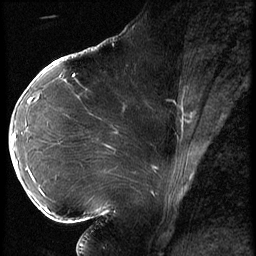
Breast MRI (dynamic contrast-enhanced), one sagittal slice. Slice 32 of 62 in the series (ordered by position). 3 images stored at this slice position (order not interpretable as contrast timing). 1.5 T. TE 4.2 ms, TR 9 ms. 256 × 256 image matrix, field of view 180 × 180 mm. Patient: female, 43 years. From the clinical record (not read from this slice): setting: breast cancer imaged before/during neoadjuvant chemotherapy; receptor status: HER2-positive.
Outlined on this slice (semi-automatic segmentation, software-assisted and operator-edited):
- analysis volume of interest (the breast-tissue region the enhancement analysis was run in; not a lesion): bounding box [x1, y1, x2, y2] px = [10, 90, 82, 203]
- tumour enhancement mask (voxels above the 140 % enhancement threshold inside the analysis volume of interest): [14, 134, 17, 163]